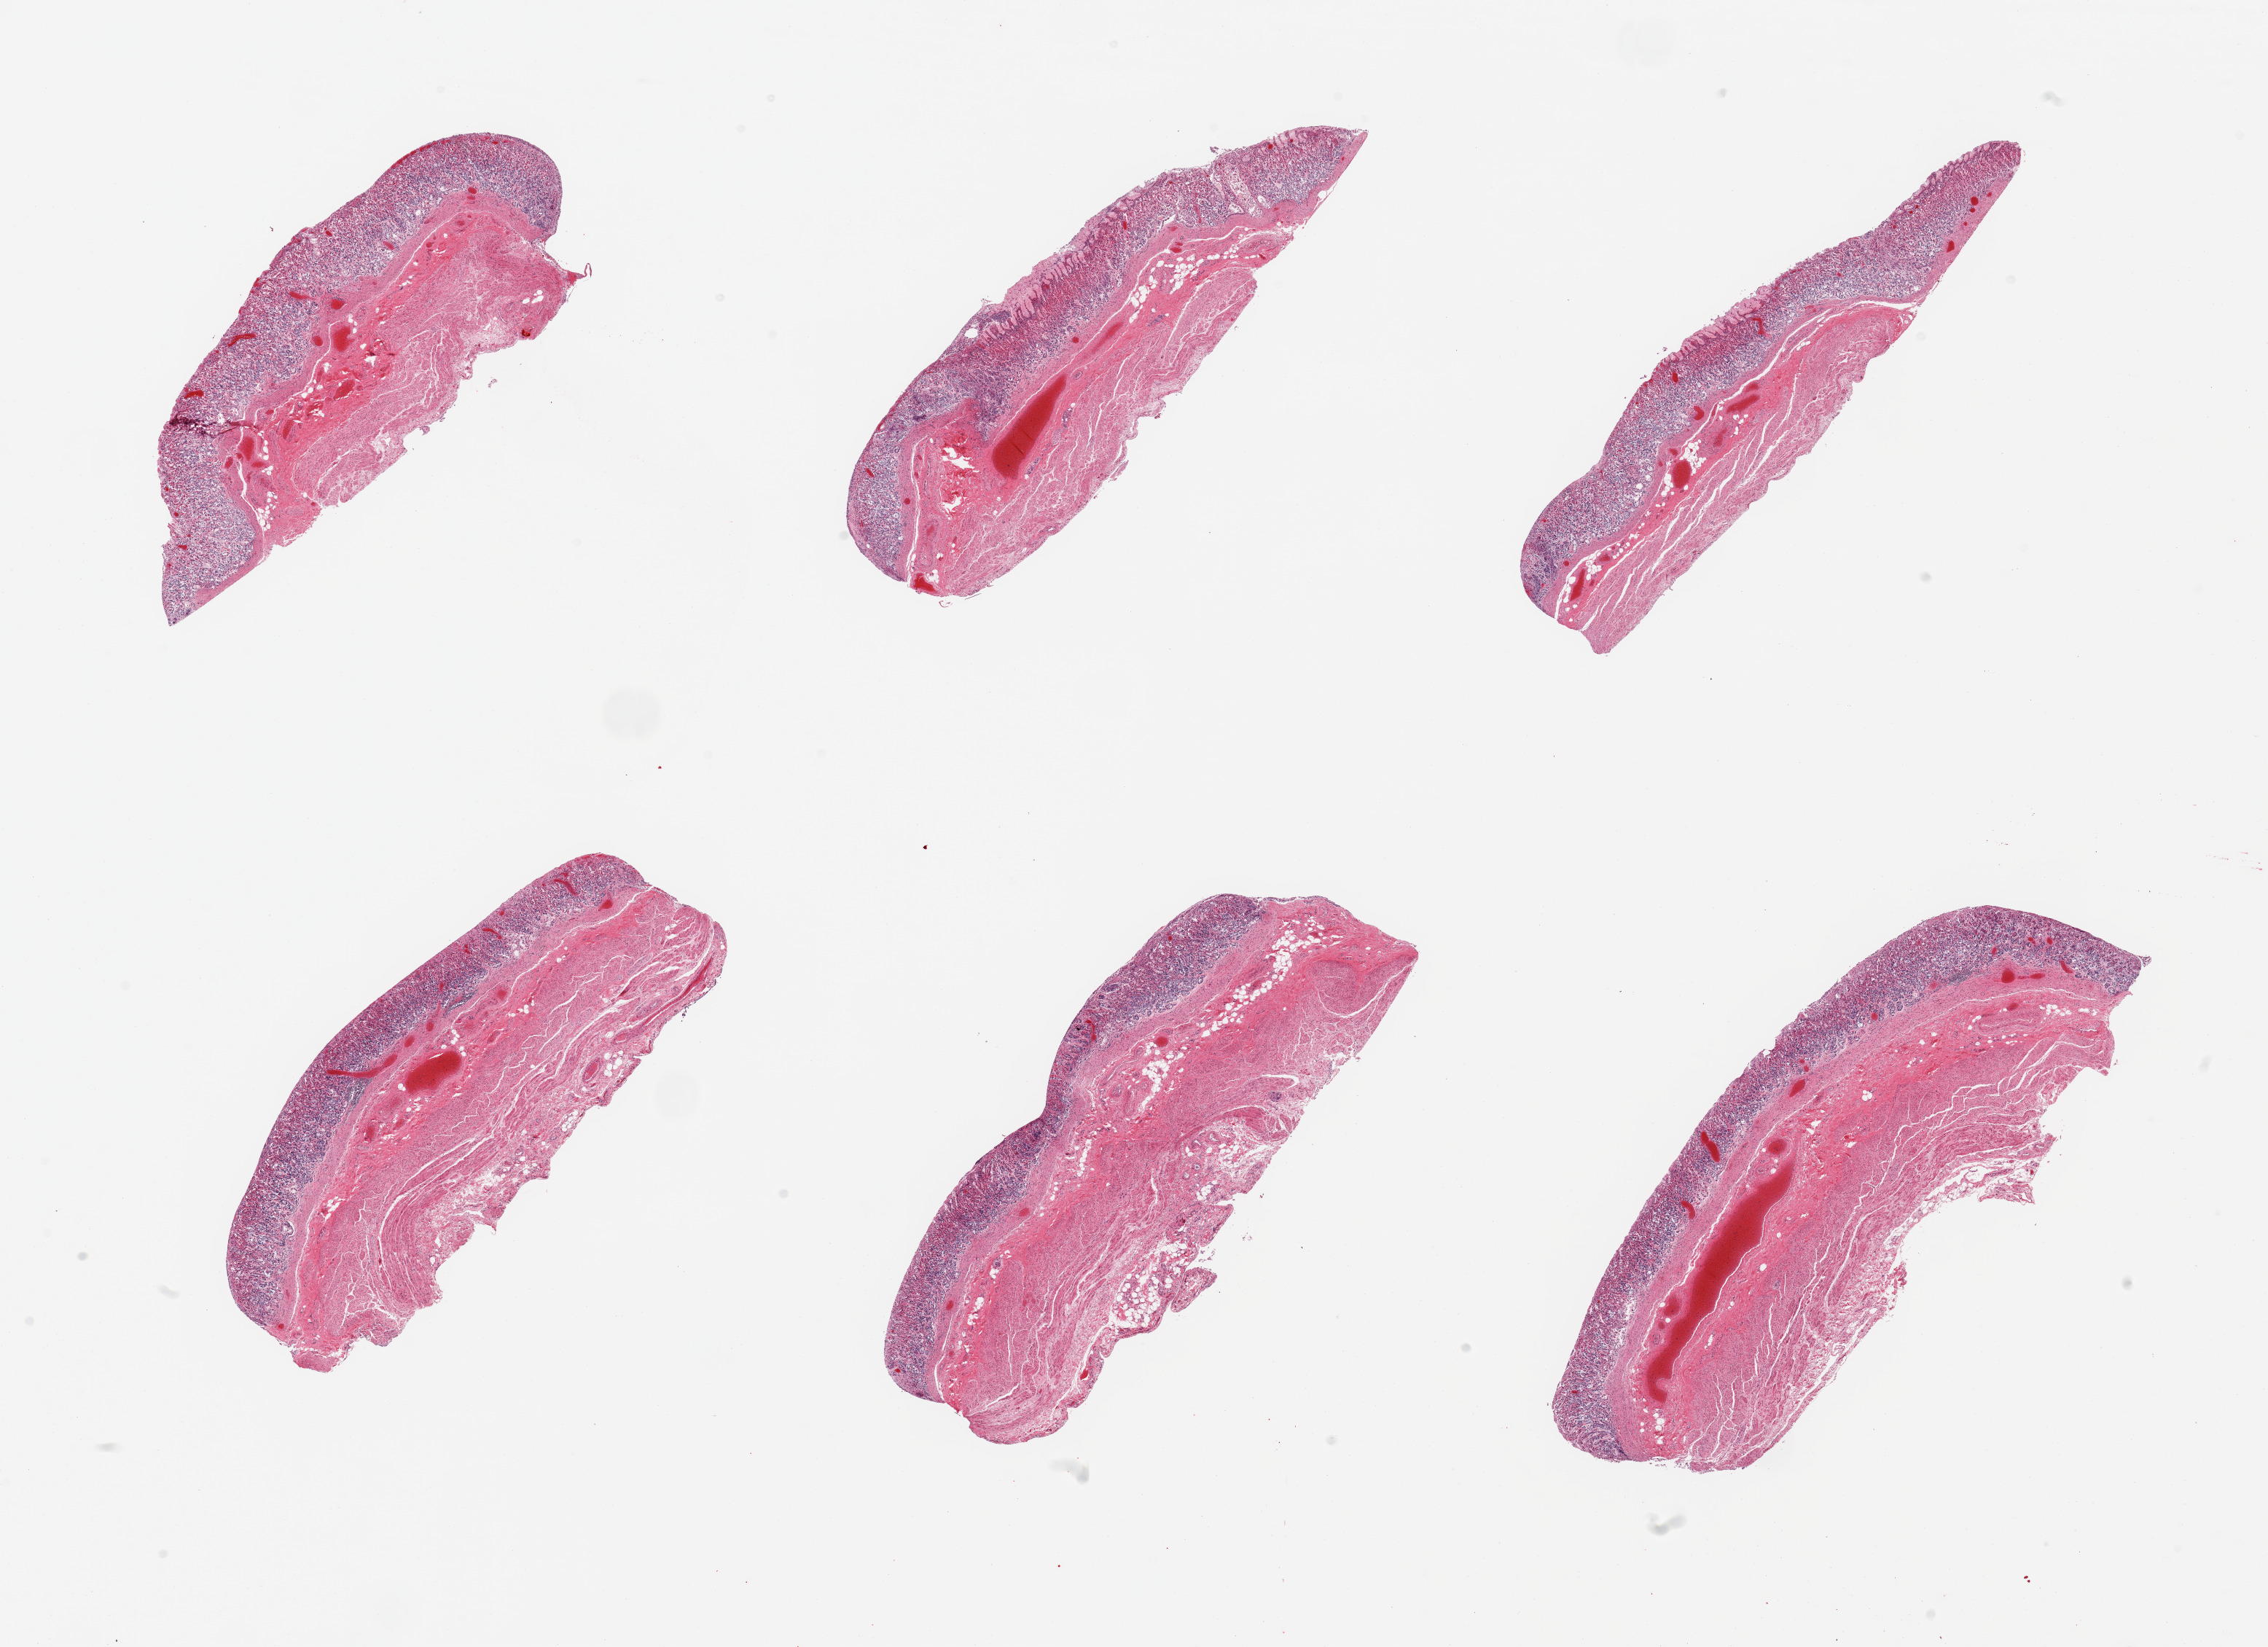
Haematoxylin and eosin whole-slide image — shown as a low-resolution overview of the whole scanned area (about 24.6 x 17.9 mm, slide scanned at 20x), PAXgene-fixed paraffin-embedded (PFPE) section, sampled site (target tissue): stomach, tissue donor sample. Donor sex: male.
Pathologist's review note for this sample: 6 pieces, mucosa up to ~0.8mm. totally autolyzed.